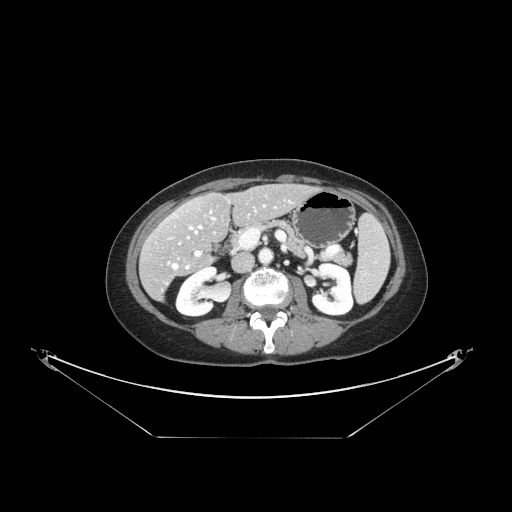
Contrast-enhanced abdominal CT, one axial slice. Position 67 of 148 along the scan axis. Reconstruction kernel STANDARD. Intravenous contrast given. Soft-tissue window (W 400 / L 40 HU). 512 × 512 image matrix. Female patient, age 73 years. From the clinical record (not read from this slice): diagnosis: colorectal cancer liver metastases, imaged before liver resection; multiple liver metastases: no; largest metastasis: 1 cm; disease in both lobes: no.
Annotated regions visible in this slice (manually delineated by an expert):
- hepatic veins: bounding box [x1, y1, x2, y2] px = [169, 201, 290, 269]
- liver: [141, 185, 313, 299]
- planned liver remnant (the part of the liver to remain after resection): [167, 185, 312, 249]
- portal vein (with intrahepatic branches): [196, 252, 200, 256]